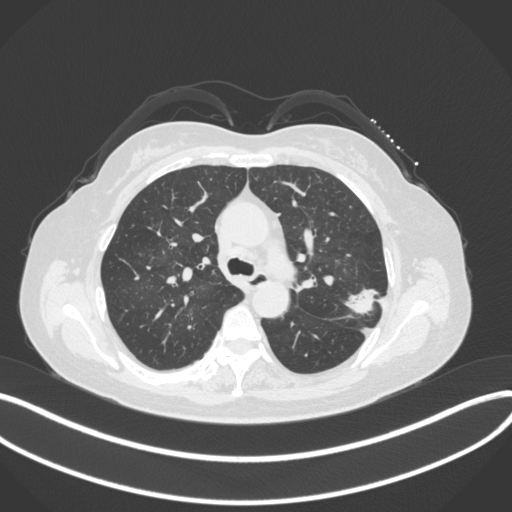
Chest CT, one axial slice. Slice 228 of 330 in the series (ordered by position). Lung window (W 1500 / L -600 HU). 1 mm slice thickness. 512 × 512 image matrix, field of view 400 × 400 mm. Female patient, age 60 years. Case-level facts recorded for this patient, not image findings: clinical TNM (as recorded): T1c N0 M0.
Structures marked on this image (rectangle marked by the reading radiologist):
- lung tumour (recorded histology: adenocarcinoma): bounding box <342,285,388,321> (left, top, right, bottom; pixels)